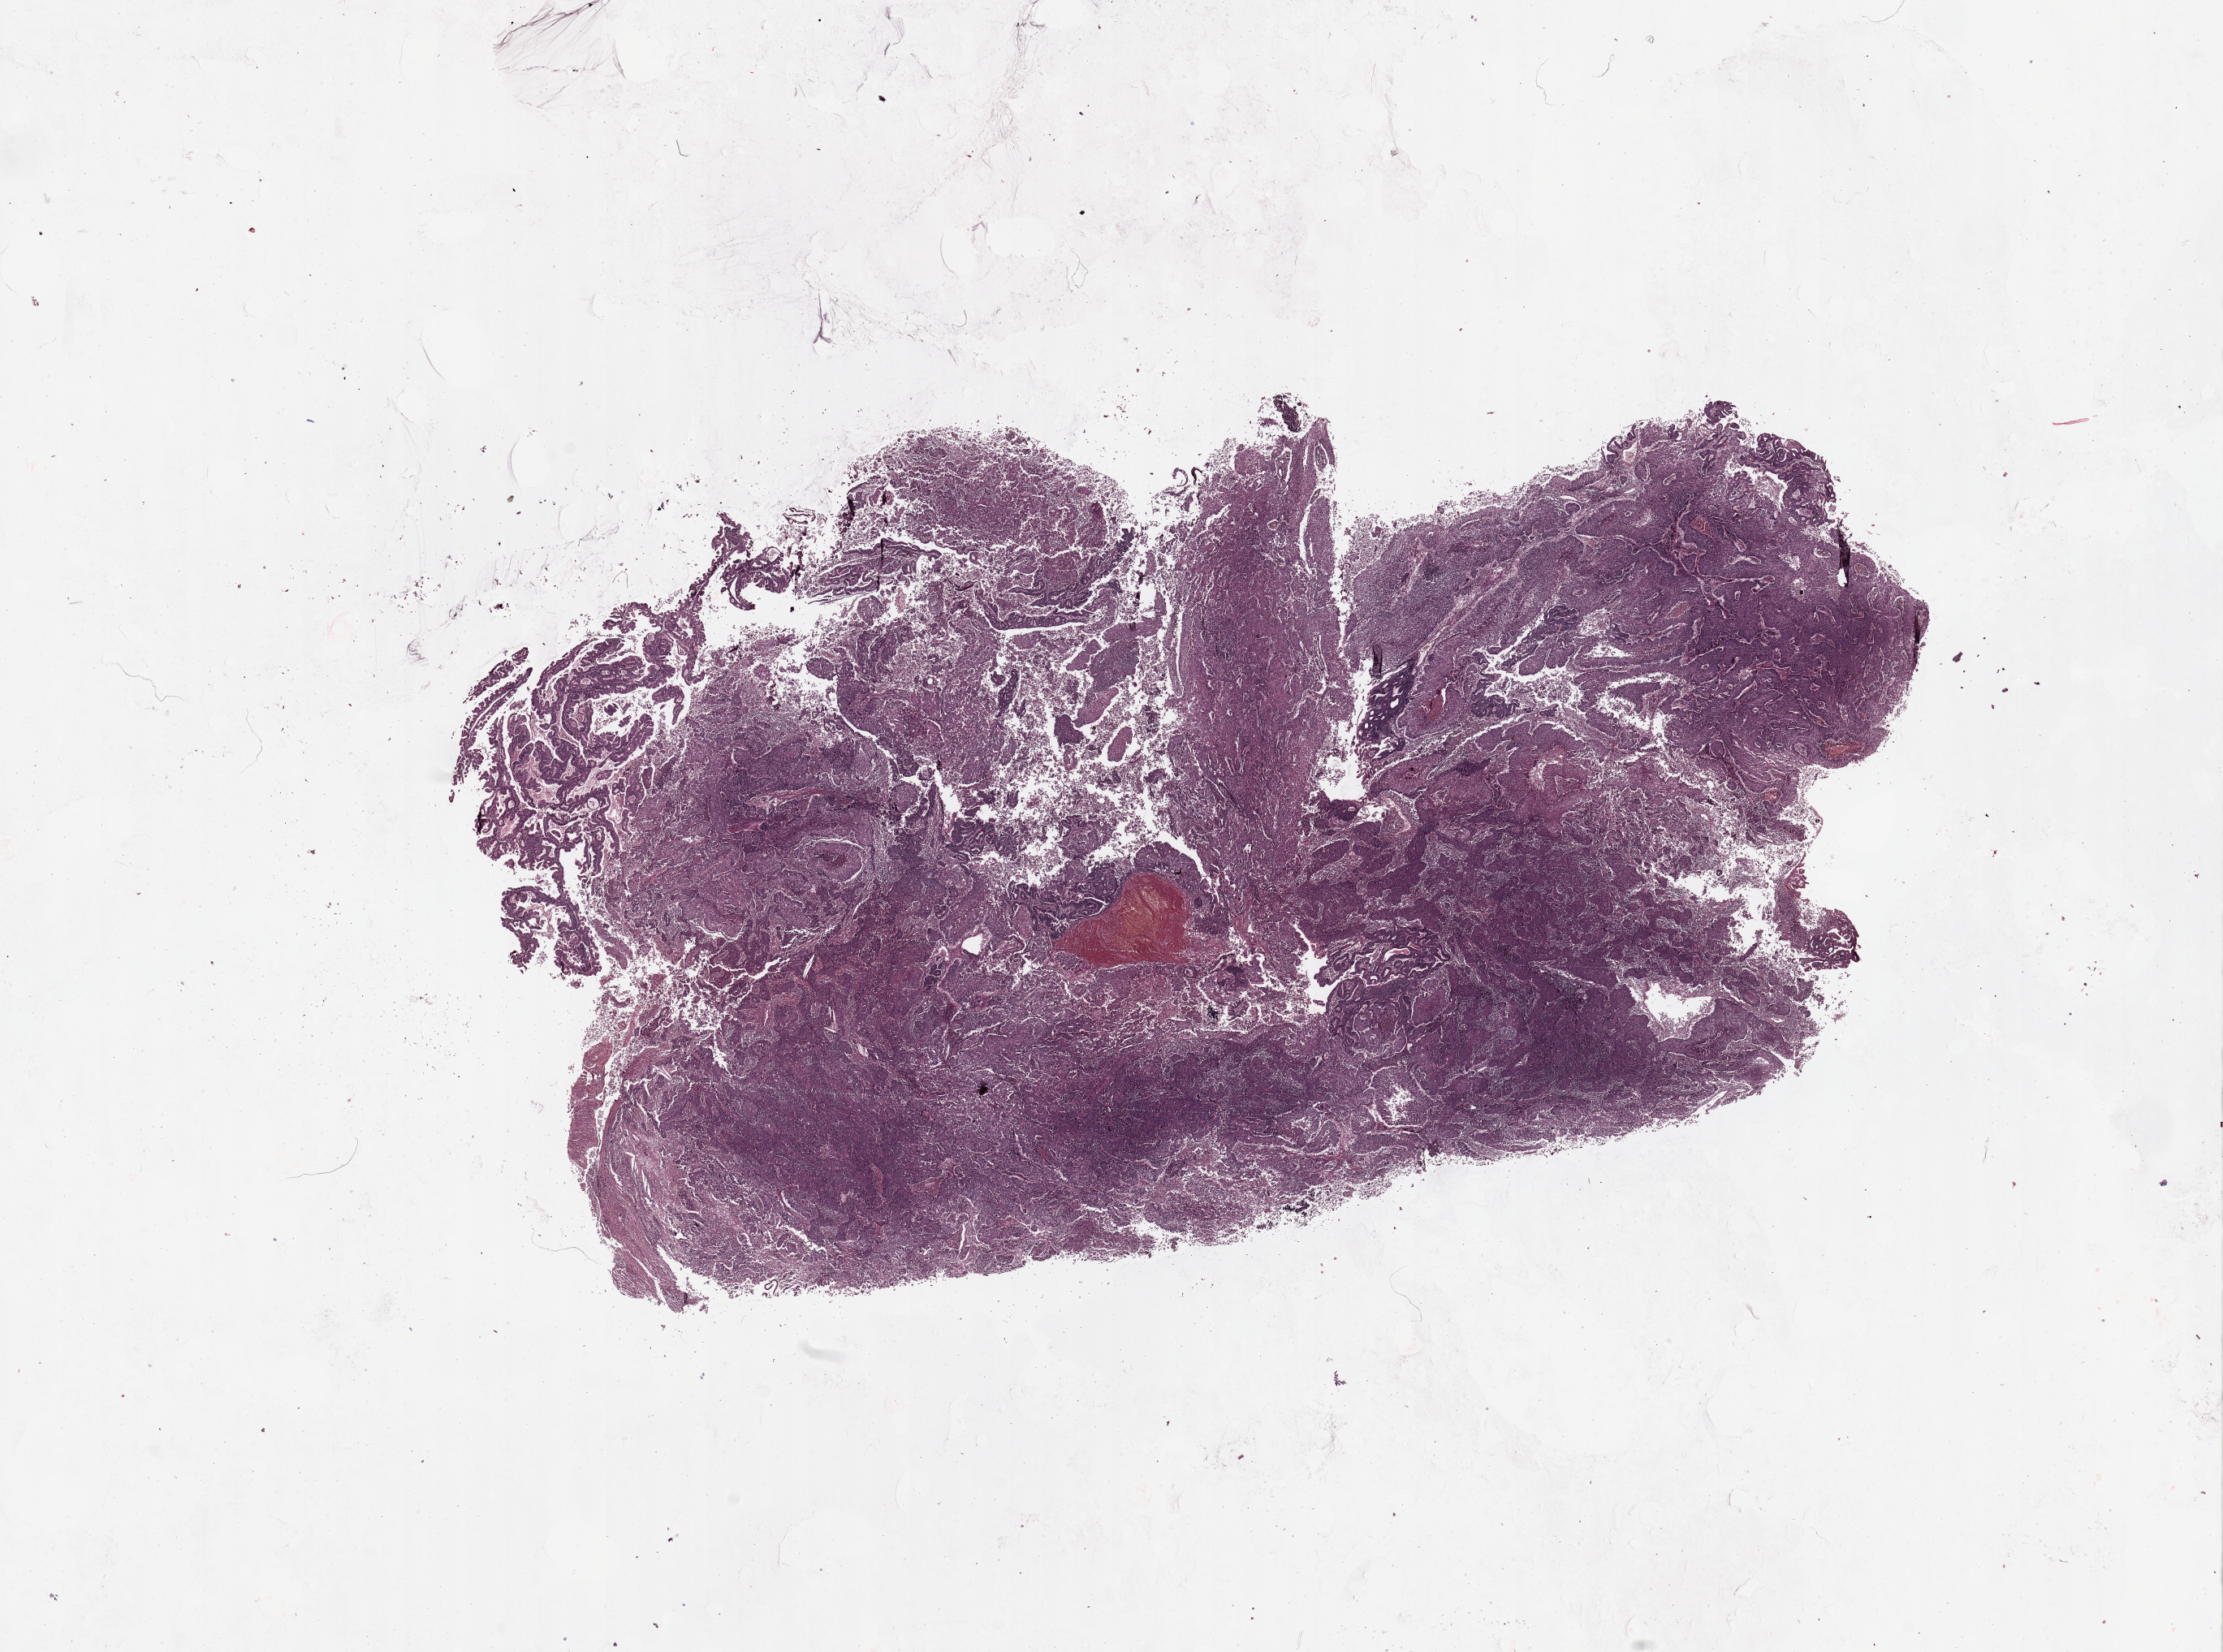
Digitized Hematoxylin and eosin (H&E) stained tissue section (whole slide), a low-resolution overview of the entire scanned area, about 21.7 x 16.1 mm (from a 20x scan). Tumour tissue sample, sampled site: uterus. Patient: female, age 58 years. Histologic grade: G3 (poorly differentiated). Composition of this section per pathologist review: tumour nuclei 85%, necrosis 5%.
Histologic diagnosis: Endometrioid adenocarcinoma, NOS. AJCC pathologic stage: III.